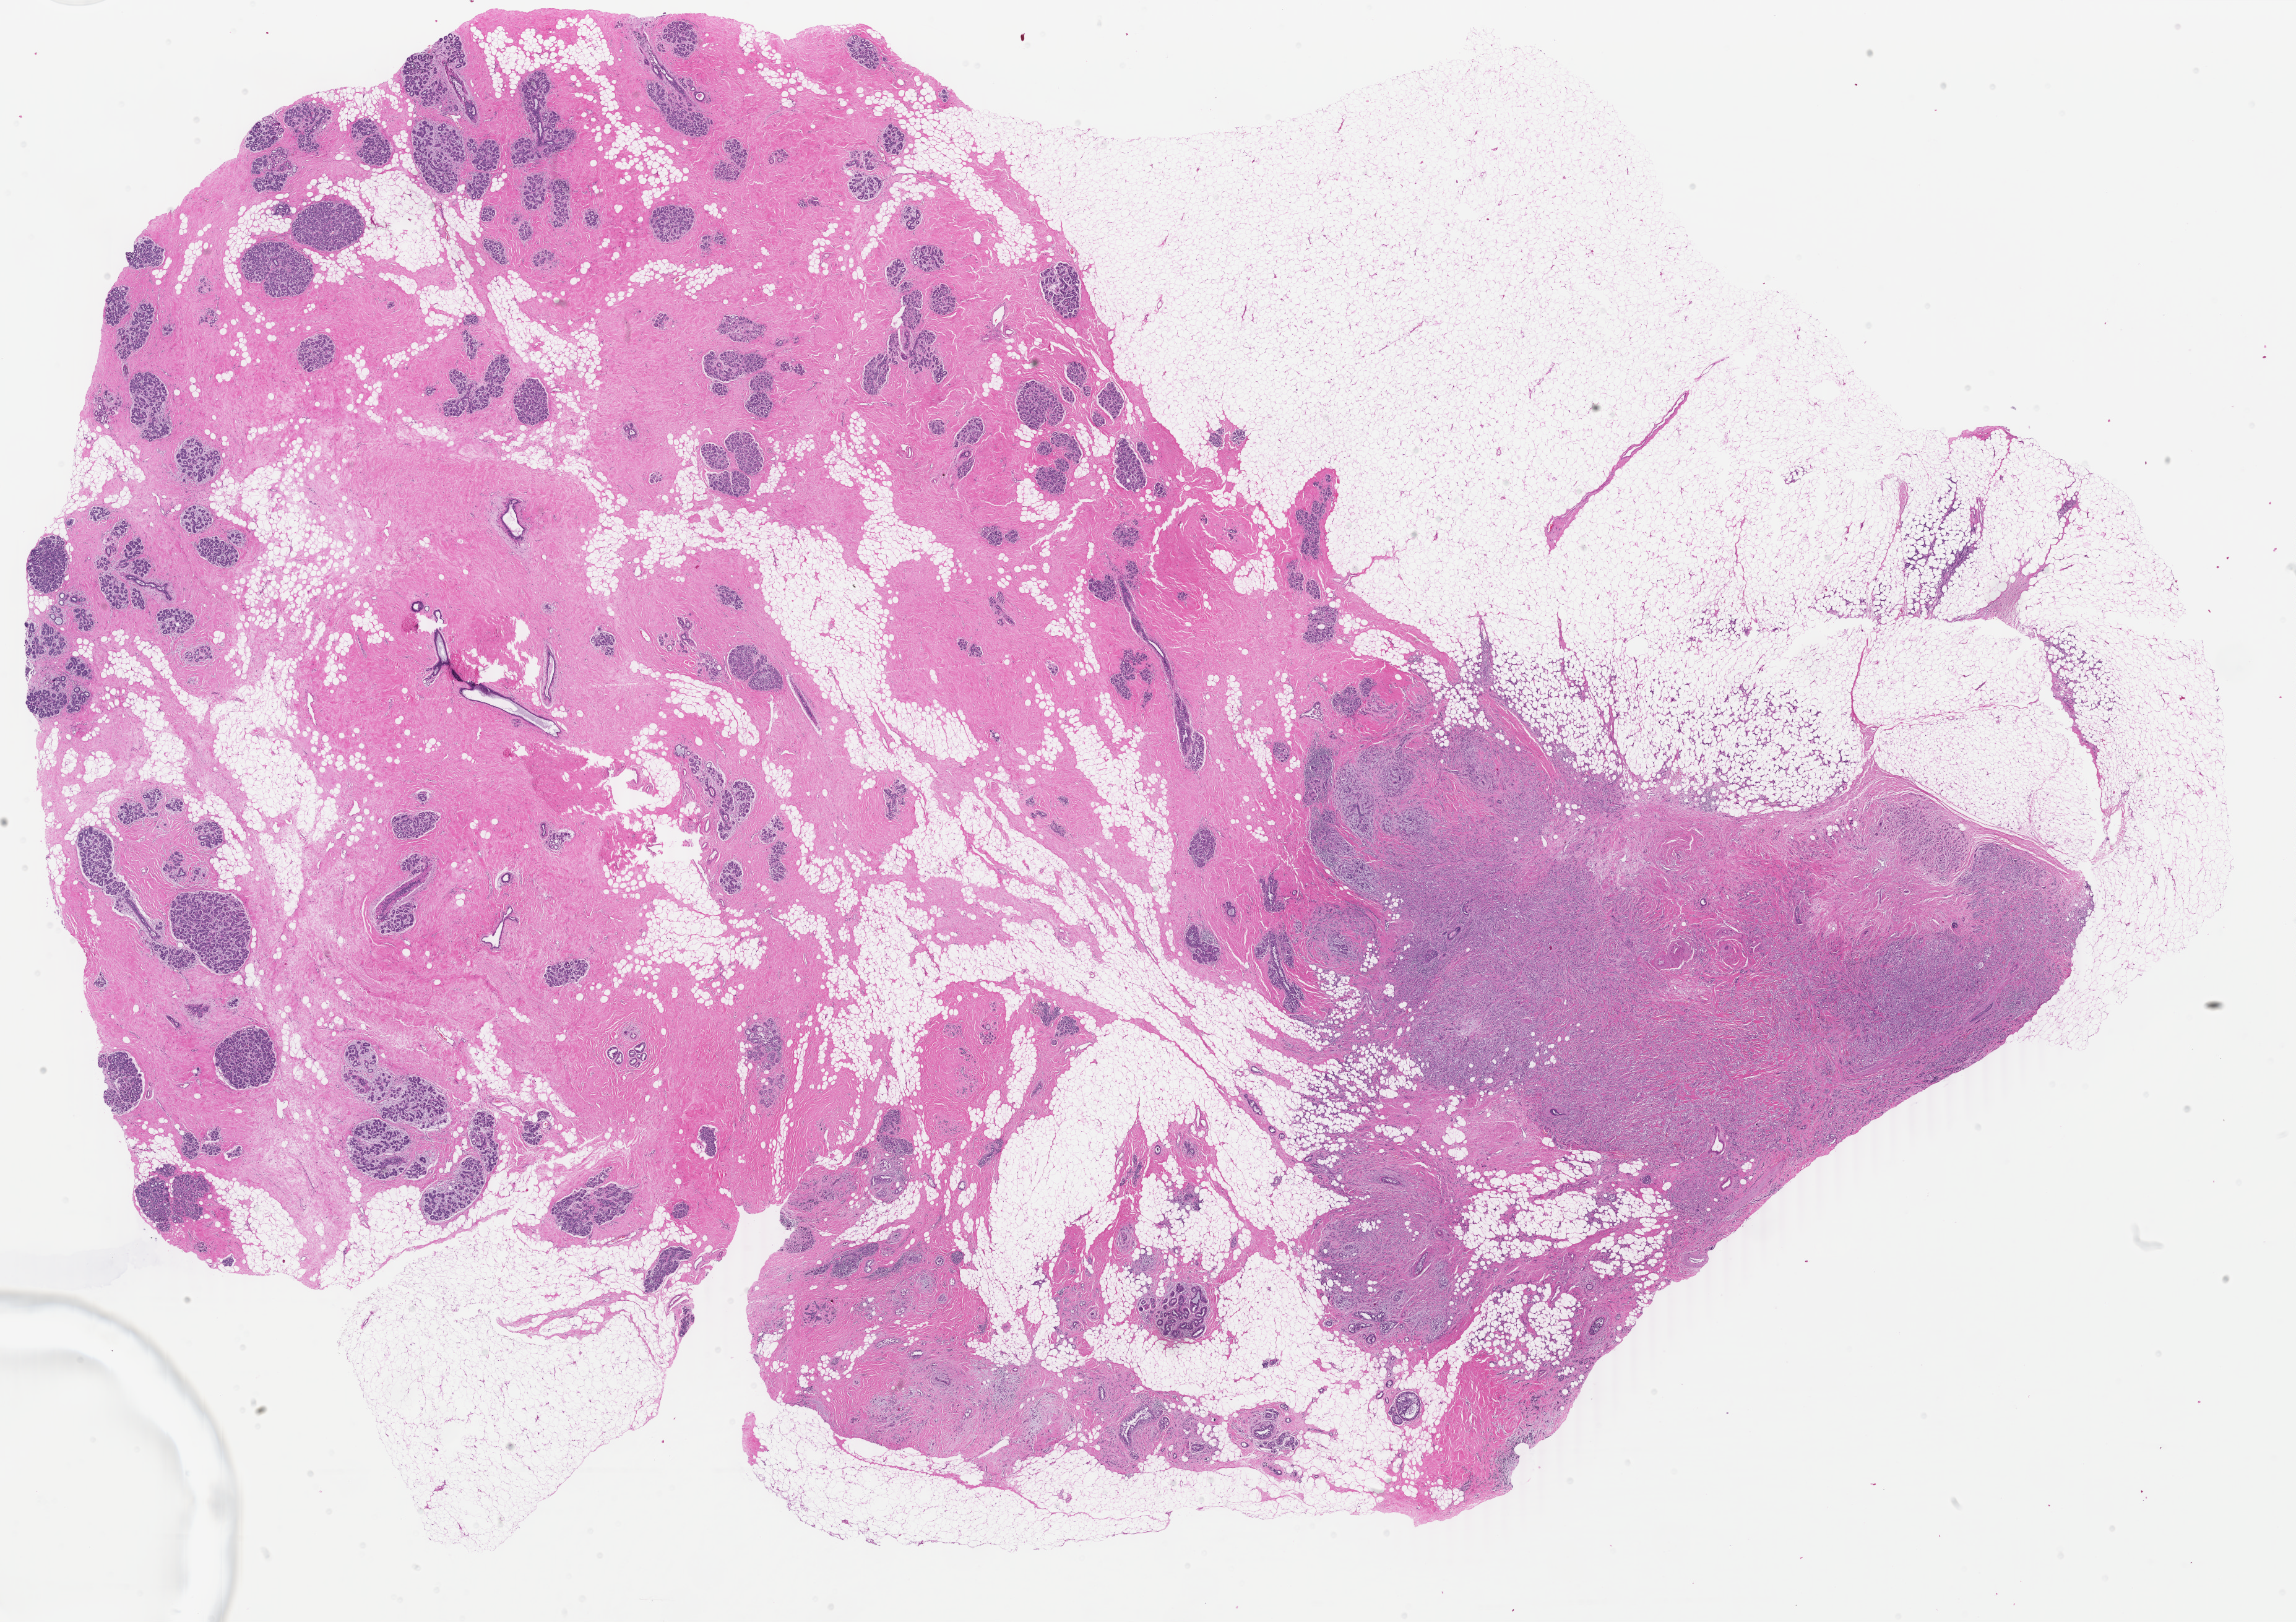
Whole-slide histology image, H&E — a low-resolution overview of the entire scanned area, about 29.5 x 20.8 mm; formalin-fixed paraffin-embedded (FFPE) diagnostic section; sample: primary tumour, breast. Patient: female, age at initial diagnosis 46 years.
Histologic diagnosis: Infiltrating duct carcinoma, NOS. Laterality: right. AJCC pathologic stage: IIA (6th edition). TNM: T2 N0 (i-) M0. Lymph nodes positive (case pathology): 0 of 2 examined.